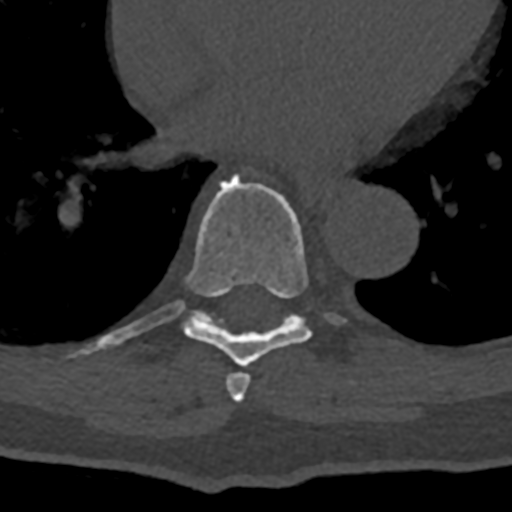
CT including the spine, one axial slice. Position 703 of 797 along the scan axis. Reconstruction kernel Br40s/3. 120 kVp. Bone window (W 1800 / L 400 HU). 512 × 512 image matrix. Male patient, age 74 years. From the clinical record (not read from this slice): primary cancer: renal; vertebrae with lytic lesions (as recorded): T10, L1, L2, L3, L4, L5.
Outlined on this slice (semi-automatically segmented with operator editing):
- T7 vertebra: bounding box (x1, y1, x2, y2) in pixels: (225, 372, 251, 403)
- T8 vertebra: (71, 172, 348, 367)
- T9 vertebra: (190, 311, 206, 320)